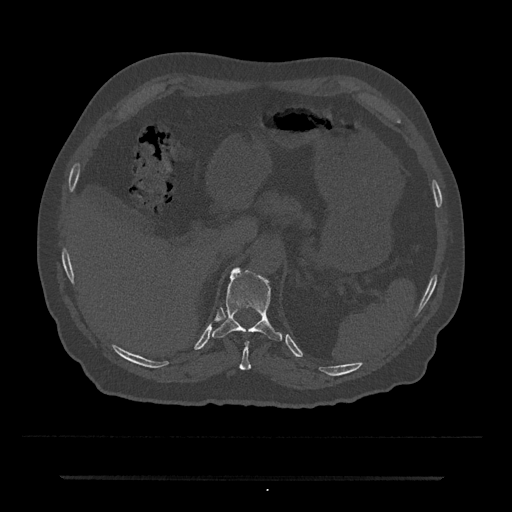
CT including the spine, one axial slice. Slice 188 of 797 in the series (ordered by position). Reconstruction kernel Br40s/3. Bone window (W 1800 / L 400 HU). 0.5 mm slice thickness. 512 × 512 image matrix, field of view 437 × 437 mm. Patient: male, 69 years. From the clinical record (not read from this slice): primary cancer: prostate.
Structures marked on this image (semi-automatically segmented with operator editing):
- T10 vertebra: box from (x=240, y=341) to (x=251, y=370) px
- T11 vertebra: (x=212, y=268)–(x=283, y=342)